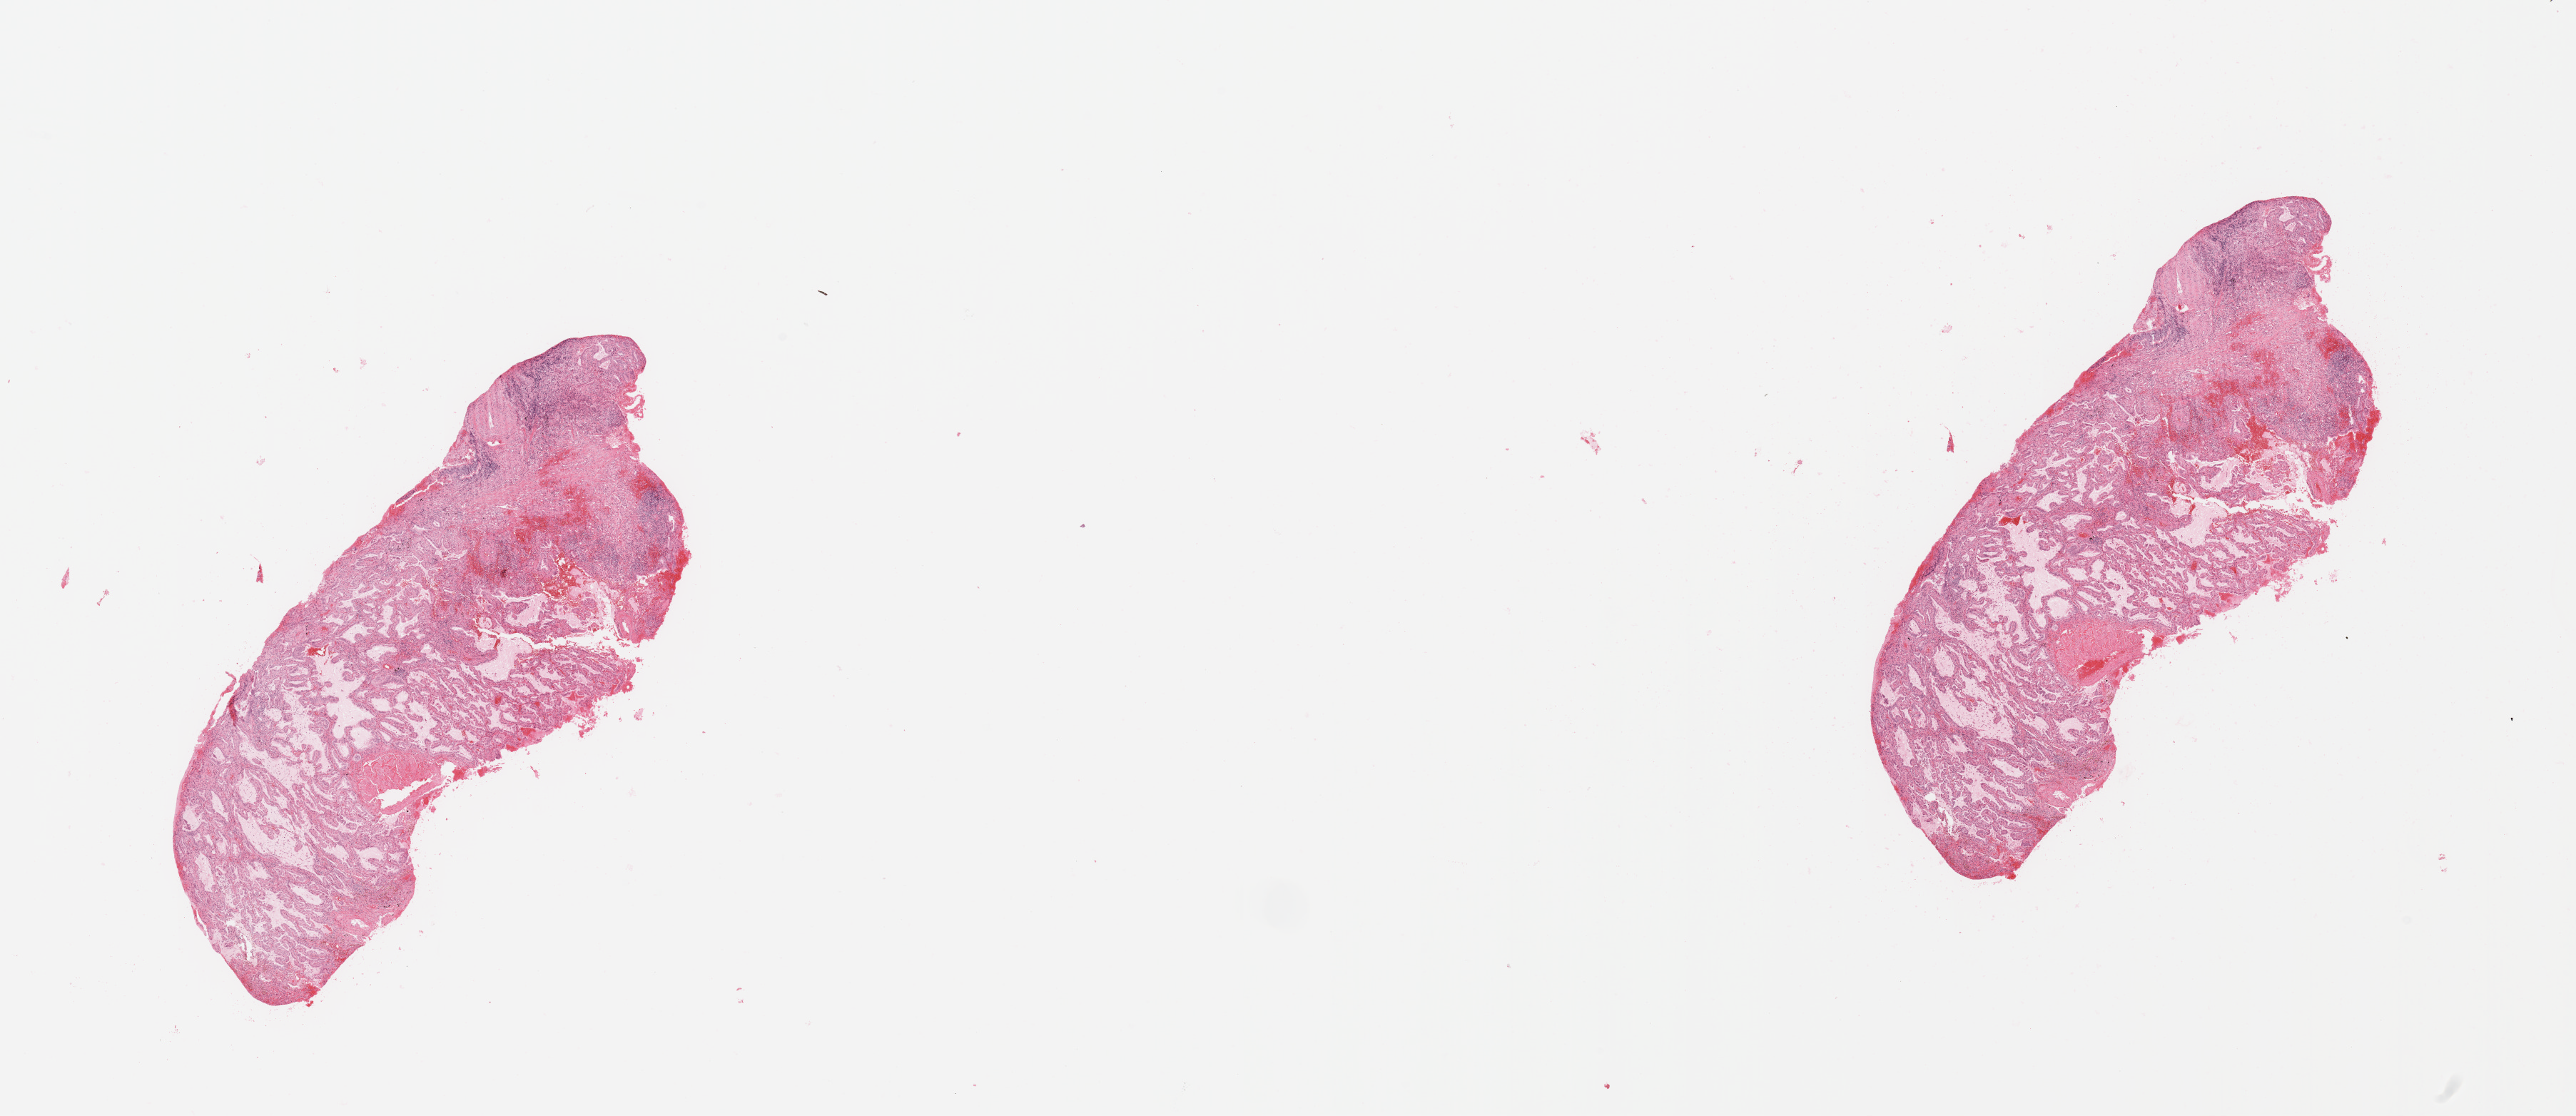
Whole-slide histology image, H&E-stained, whole scanned area (about 28.5 x 12.4 mm, from a 20x scan) shown as a low-resolution overview. Tumour tissue sample, sampled site: lung. Male, 67 y/o. Histologic grade: G1 (well differentiated). Pathologist review of this section (percent, as recorded): tumour nuclei 70%, necrosis 0%.
AJCC pathologic stage: IA. Diagnosis: Adenocarcinoma, NOS.